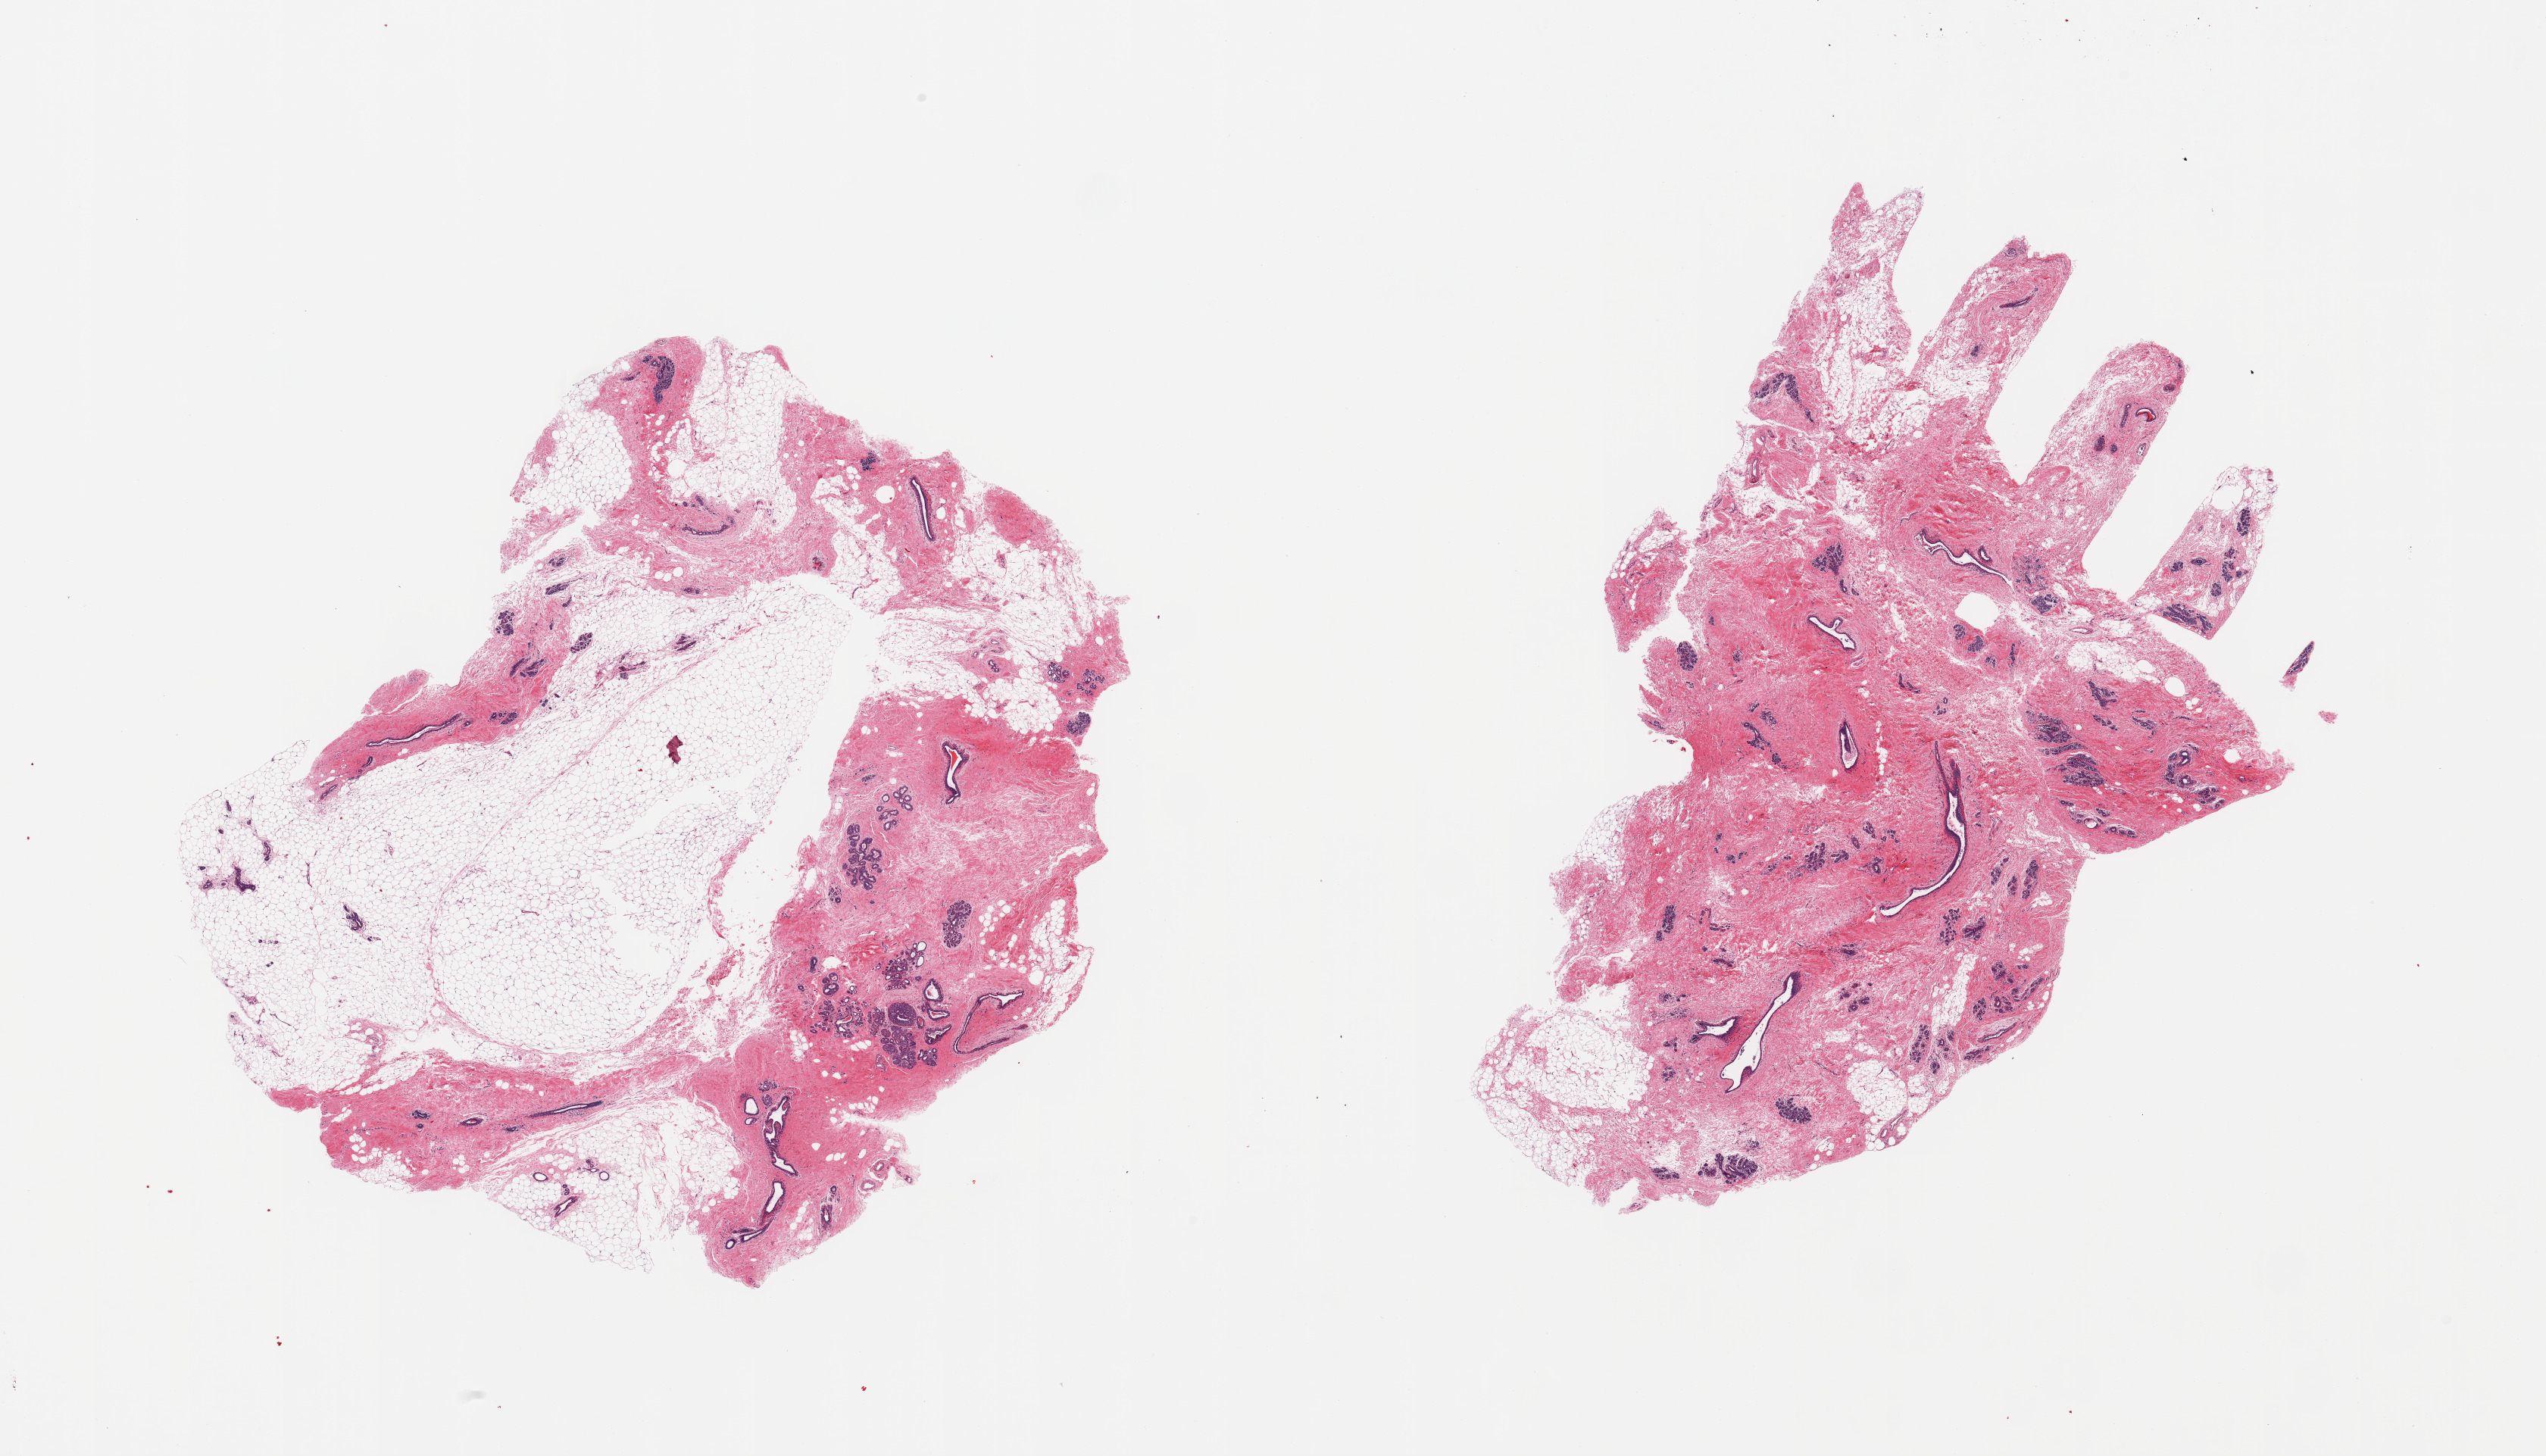
Digitized haematoxylin and eosin-stained section, brightfield, shown as a low-resolution overview of the whole scanned area (about 26.6 x 15.2 mm), PAXgene-fixed, paraffin-embedded tissue, target tissue: breast, tissue donor sample. Female donor.
Review note (as recorded): 2 pieces; ductal and lobular units present; focus of lobular hyperplasia.